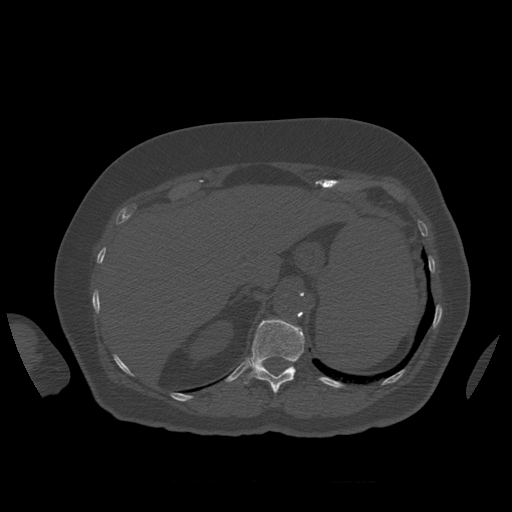
CT including the spine, one axial slice. Slice 300 of 399 in the series (ordered by position). 120 kVp. Bone window (W 1800 / L 400 HU). 1.25 mm slice thickness. 512 × 512 image matrix. Patient age 81 years. From the clinical record (not read from this slice): primary cancer: renal; vertebrae with lytic lesions (as recorded): L1.
Outlined on this slice (semi-automatically segmented with operator editing):
- L1 vertebra: bounding box <293,366,295,368> (left, top, right, bottom; pixels)
- T12 vertebra: <244,319,305,394>